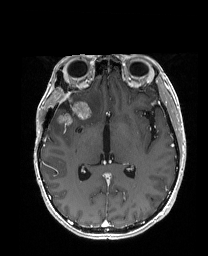
Brain MRI from a brain-tumour surgery series, one axial slice. Slice 96 of 192 in the series (ordered by position). T1-weighted post-contrast. 208 × 256 image matrix, field of view 203 × 250 mm. From the clinical record (not read from this slice): histopathology: Metastatic Carcinoma from Breast primary; tumour location: Right Frontal.
Outlined on this slice (manually delineated by an expert):
- previous resection cavity: bounding box <60,103,71,112> (left, top, right, bottom; pixels)
- tumour: <55,96,104,124>